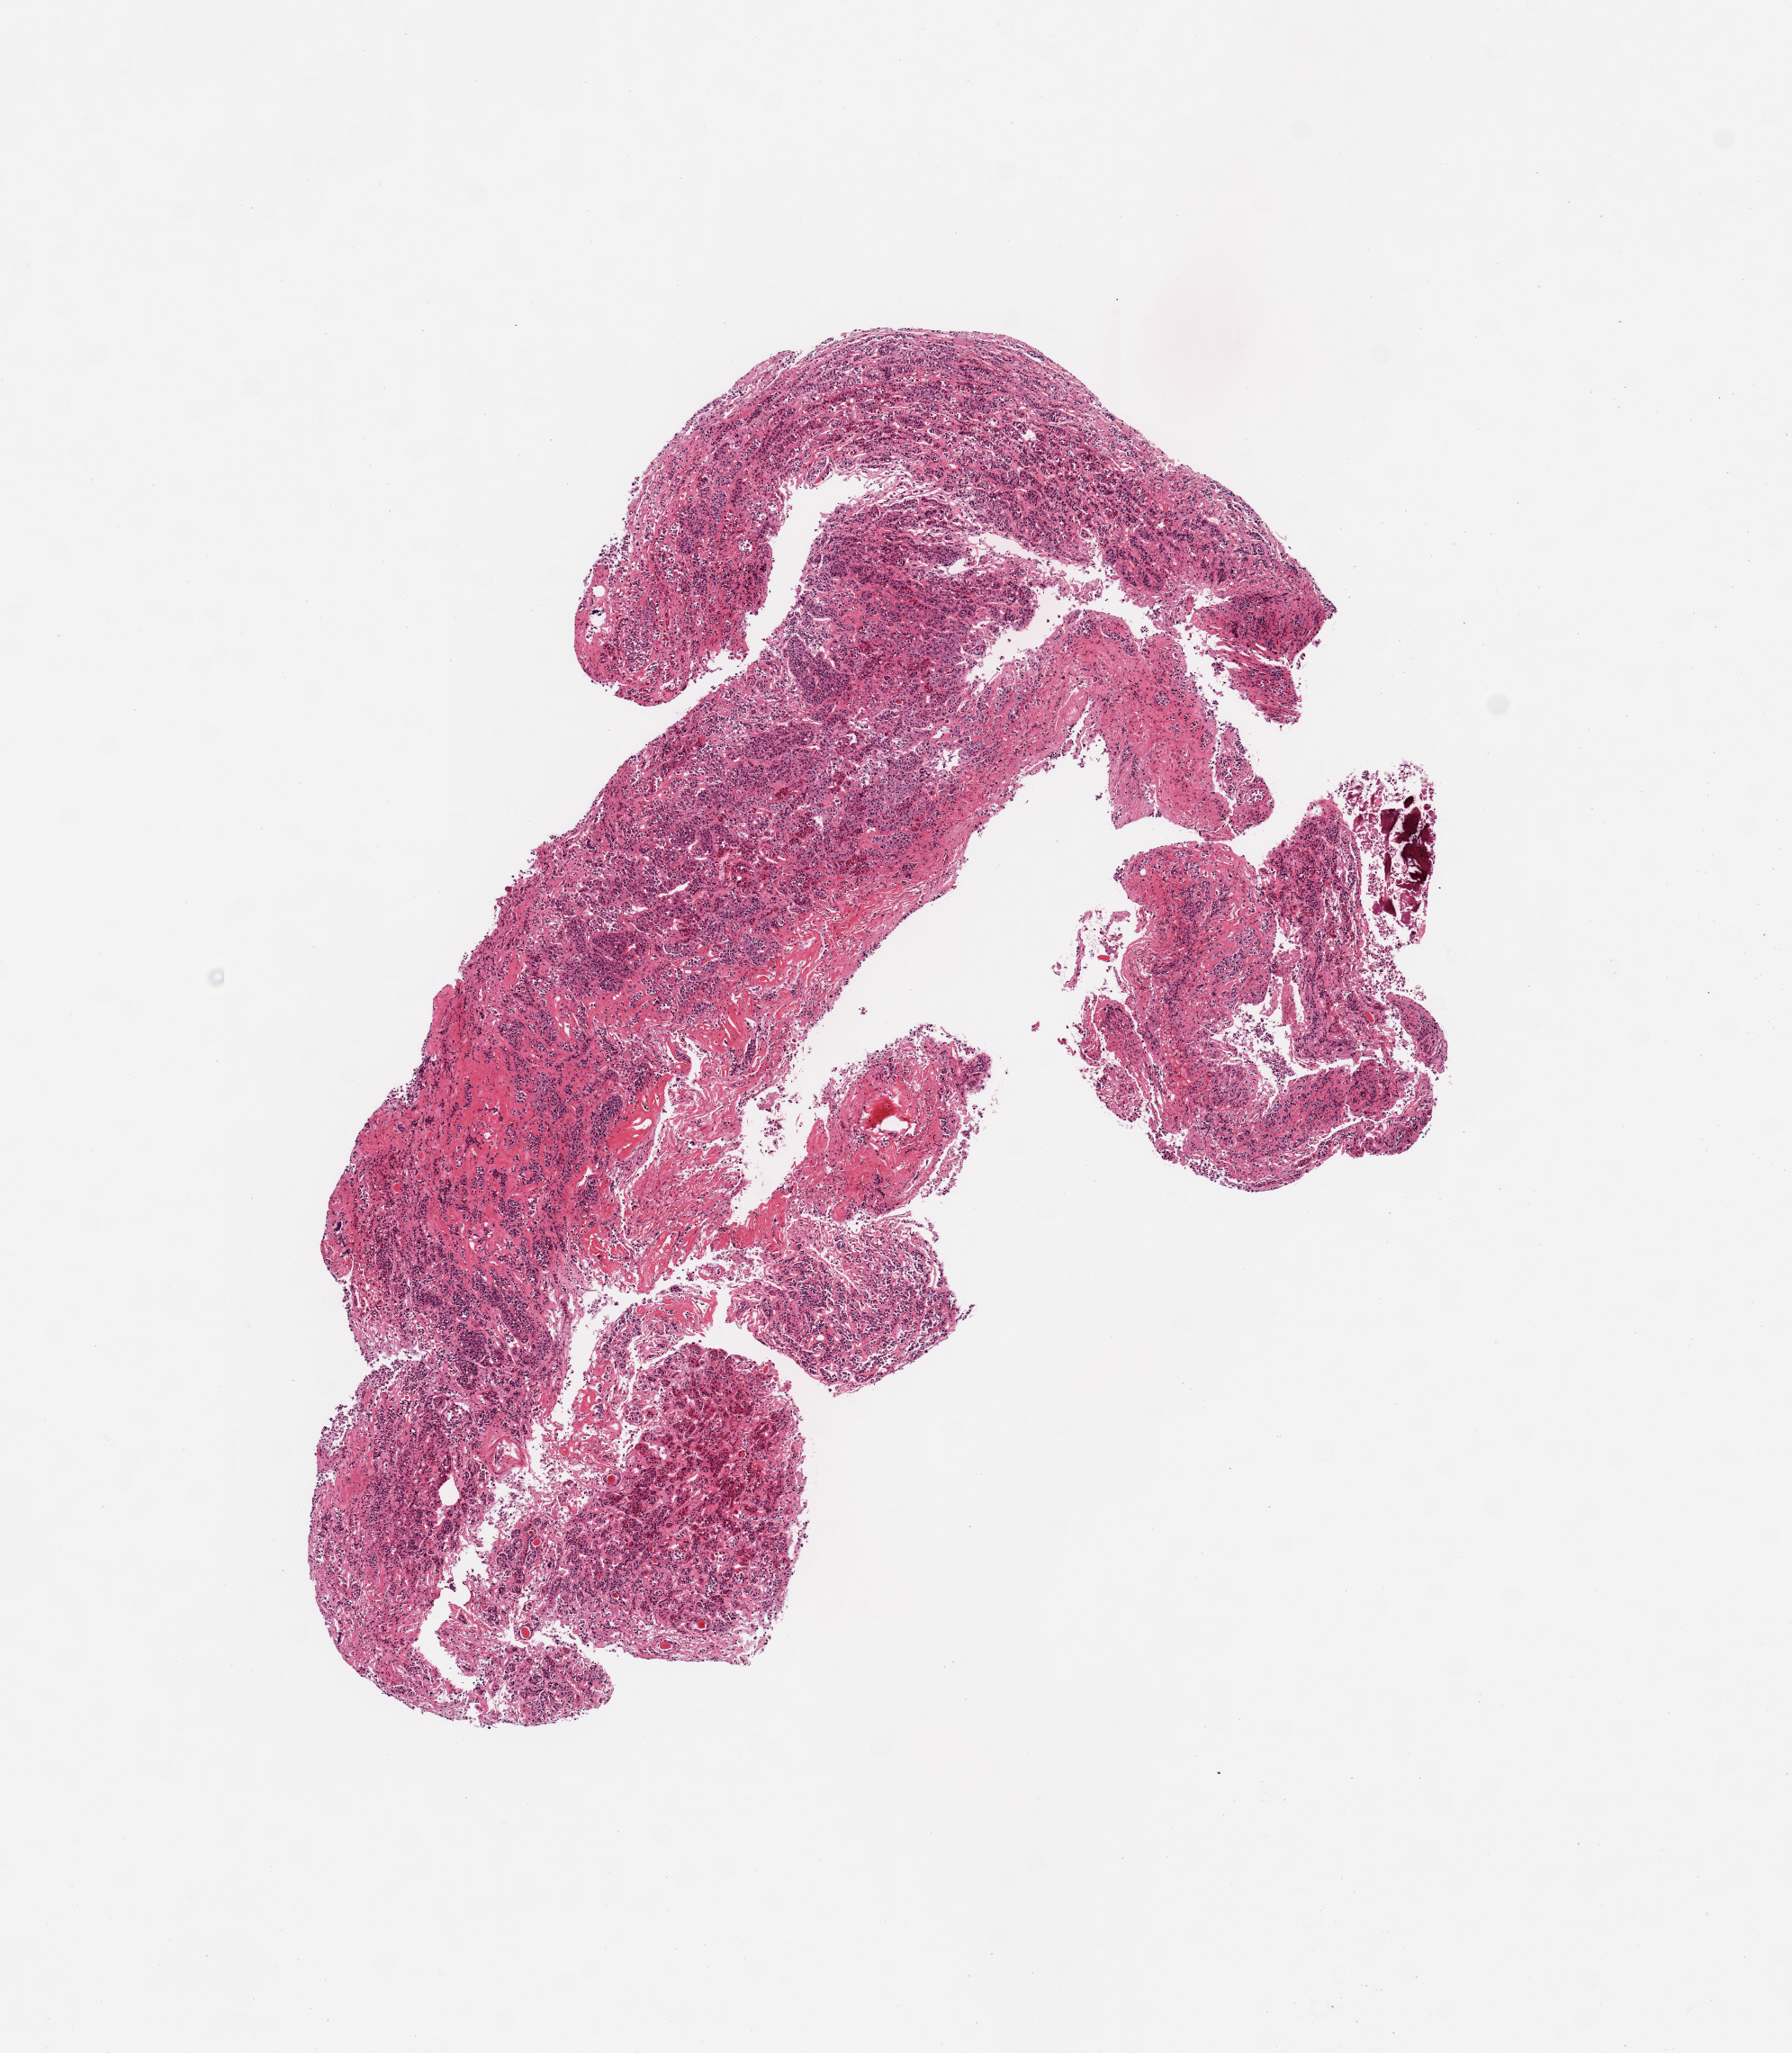
Whole-slide image, H&E stain — shown as a low-resolution overview of the whole scanned area (about 7.9 x 9.0 mm), PAXgene-fixed paraffin-embedded (PFPE) section, section of pituitary (target tissue), tissue donor sample. Donor: female.
- reviewer comment on this tissue sample: 1 fragmented piece